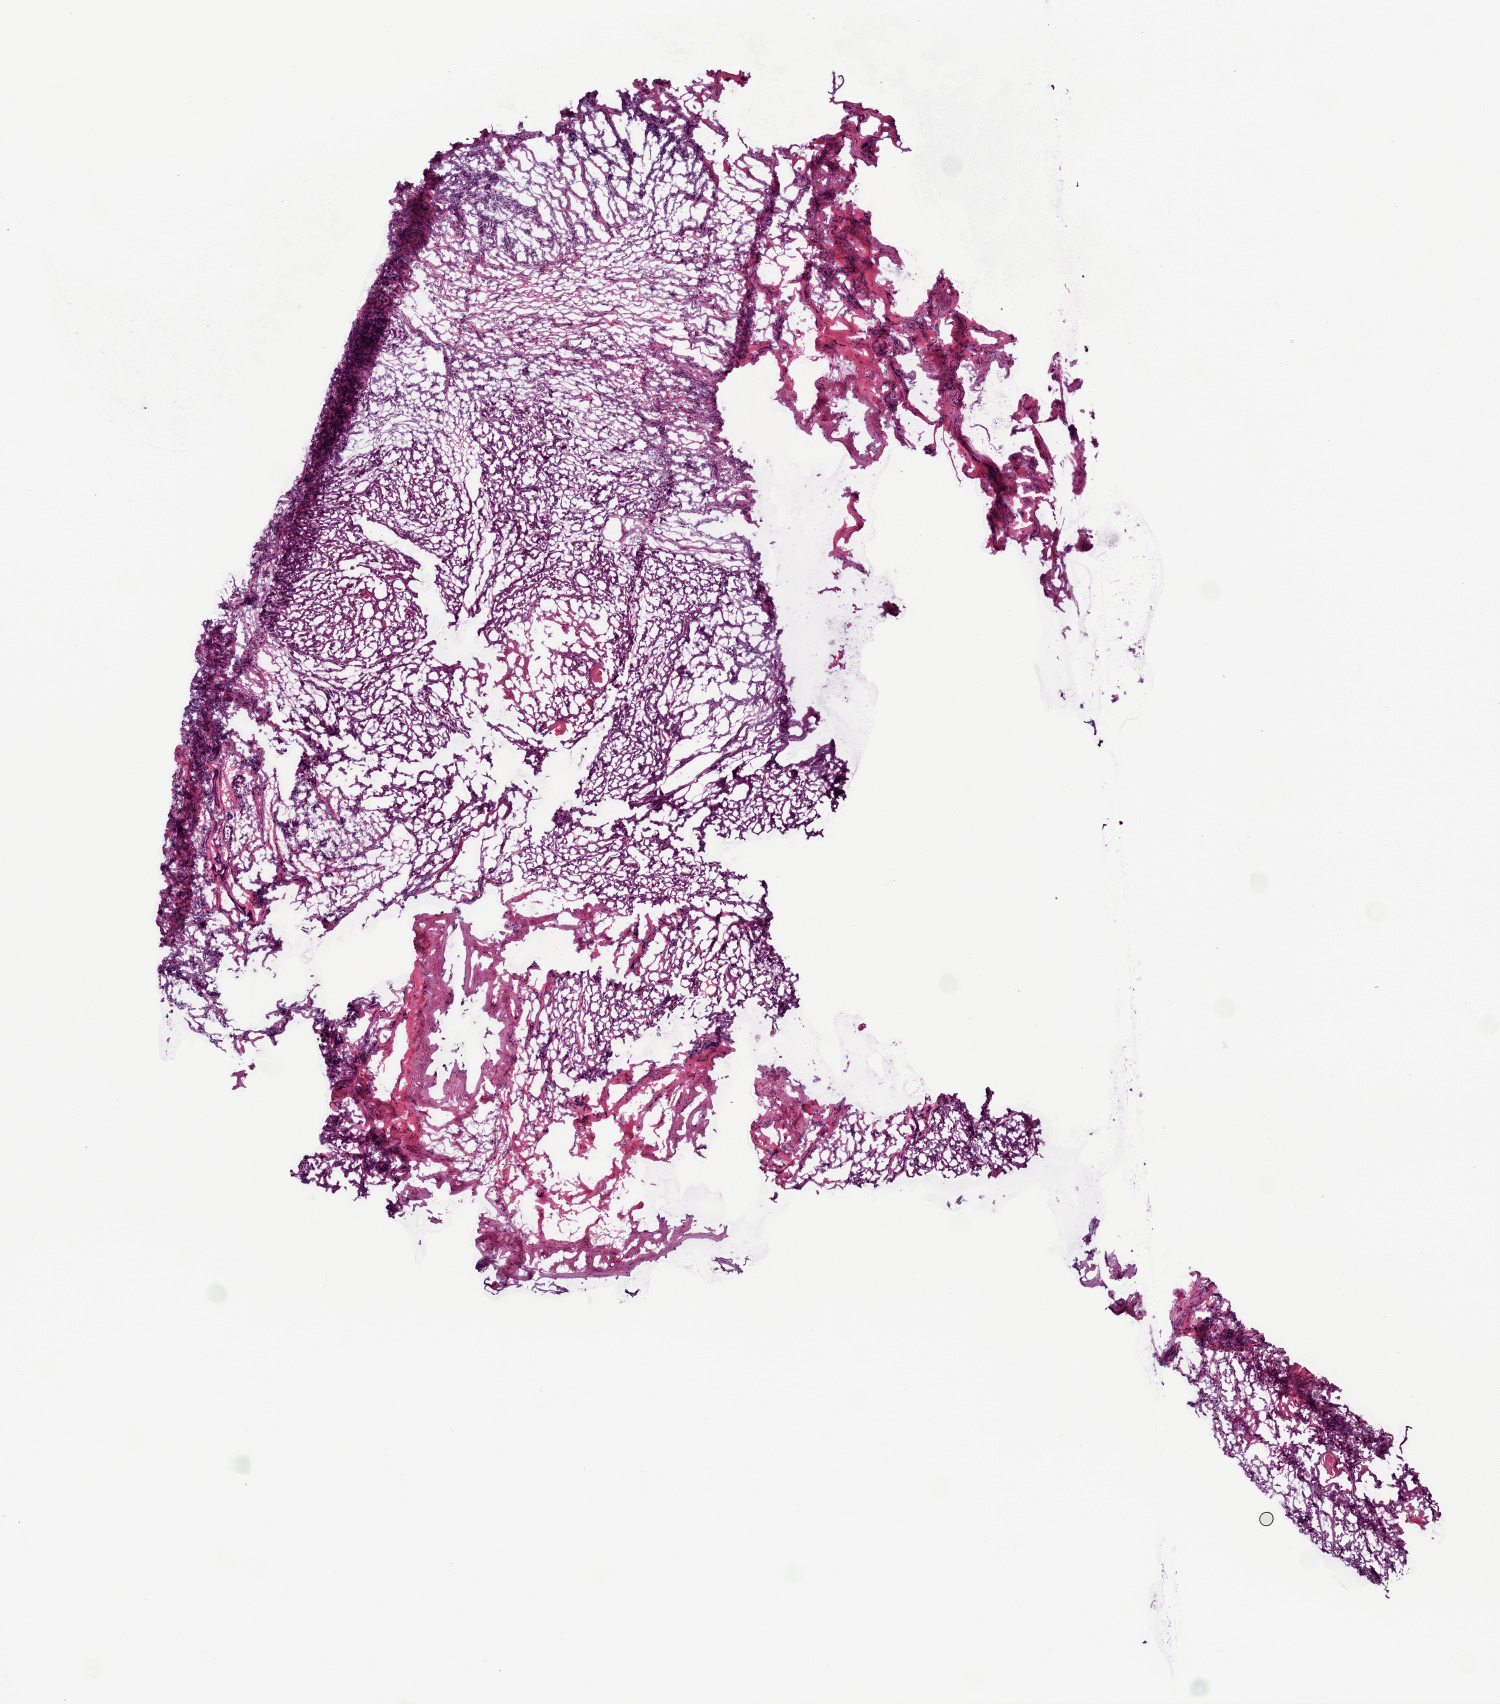
Whole-slide histology image, Hematoxylin and eosin (H&E) stained — low-resolution overview of the scanned area, about 6.0 x 6.8 mm; frozen section; sample: primary tumour, head and neck. Patient: male, age at initial diagnosis 65 years. Slide review estimates, as recorded: tumour cells 65%, tumour nuclei 60%.
Diagnosis: Squamous cell carcinoma, NOS (floor of mouth, NOS).